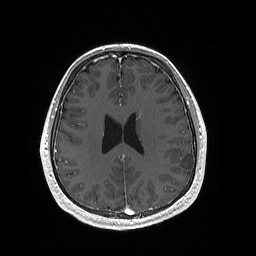
Brain MRI from a brain-tumour surgery series, one axial slice; slice 81 of 192 in the series (ordered by position); T1-weighted post-contrast; 1 mm slice thickness; 256 × 256 image matrix, field of view 256 × 256 mm. Case-level facts recorded for this patient, not image findings: histopathology: Dysembryoplastic neuroepithelial tumor; WHO grade: 1; IDH mutation: no.
Outlined on this slice (expert manual segmentation):
- tumour: bounding box <180,161,188,166> (left, top, right, bottom; pixels)